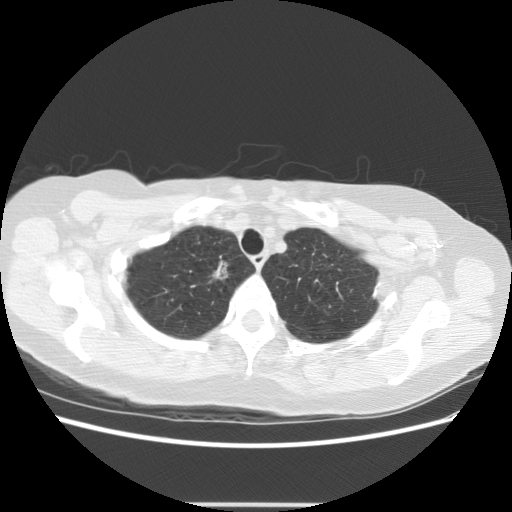
Low-dose screening chest CT, one axial slice. Slice 108 of 126 in the series (ordered by position). Reconstruction kernel STANDARD. Lung window (W 1500 / L -600 HU). 2.5 mm slice thickness. 512 × 512 image matrix, field of view 360 × 360 mm.
Annotated regions visible in this slice (manually delineated by an expert):
- lesion 1 (tumor, upper lobe of right lung): box from (x=212, y=260) to (x=229, y=279) px